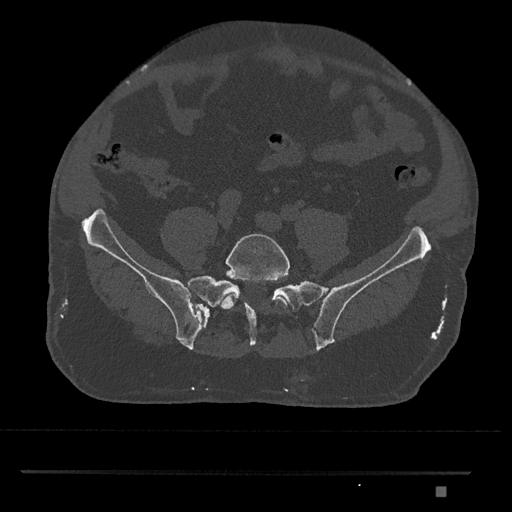
CT including the spine, one axial slice; slice 531 of 1134 in the series (ordered by position); 120 kVp; bone window (W 1800 / L 400 HU); 512 × 512 image matrix, field of view 429 × 429 mm. Patient: male, 65 years. From the clinical record (not read from this slice): primary cancer: prostate.
Structures marked on this image (semi-automatic segmentation, software-assisted and operator-edited):
- L5 vertebra: bounding box <221,233,290,312> (left, top, right, bottom; pixels)